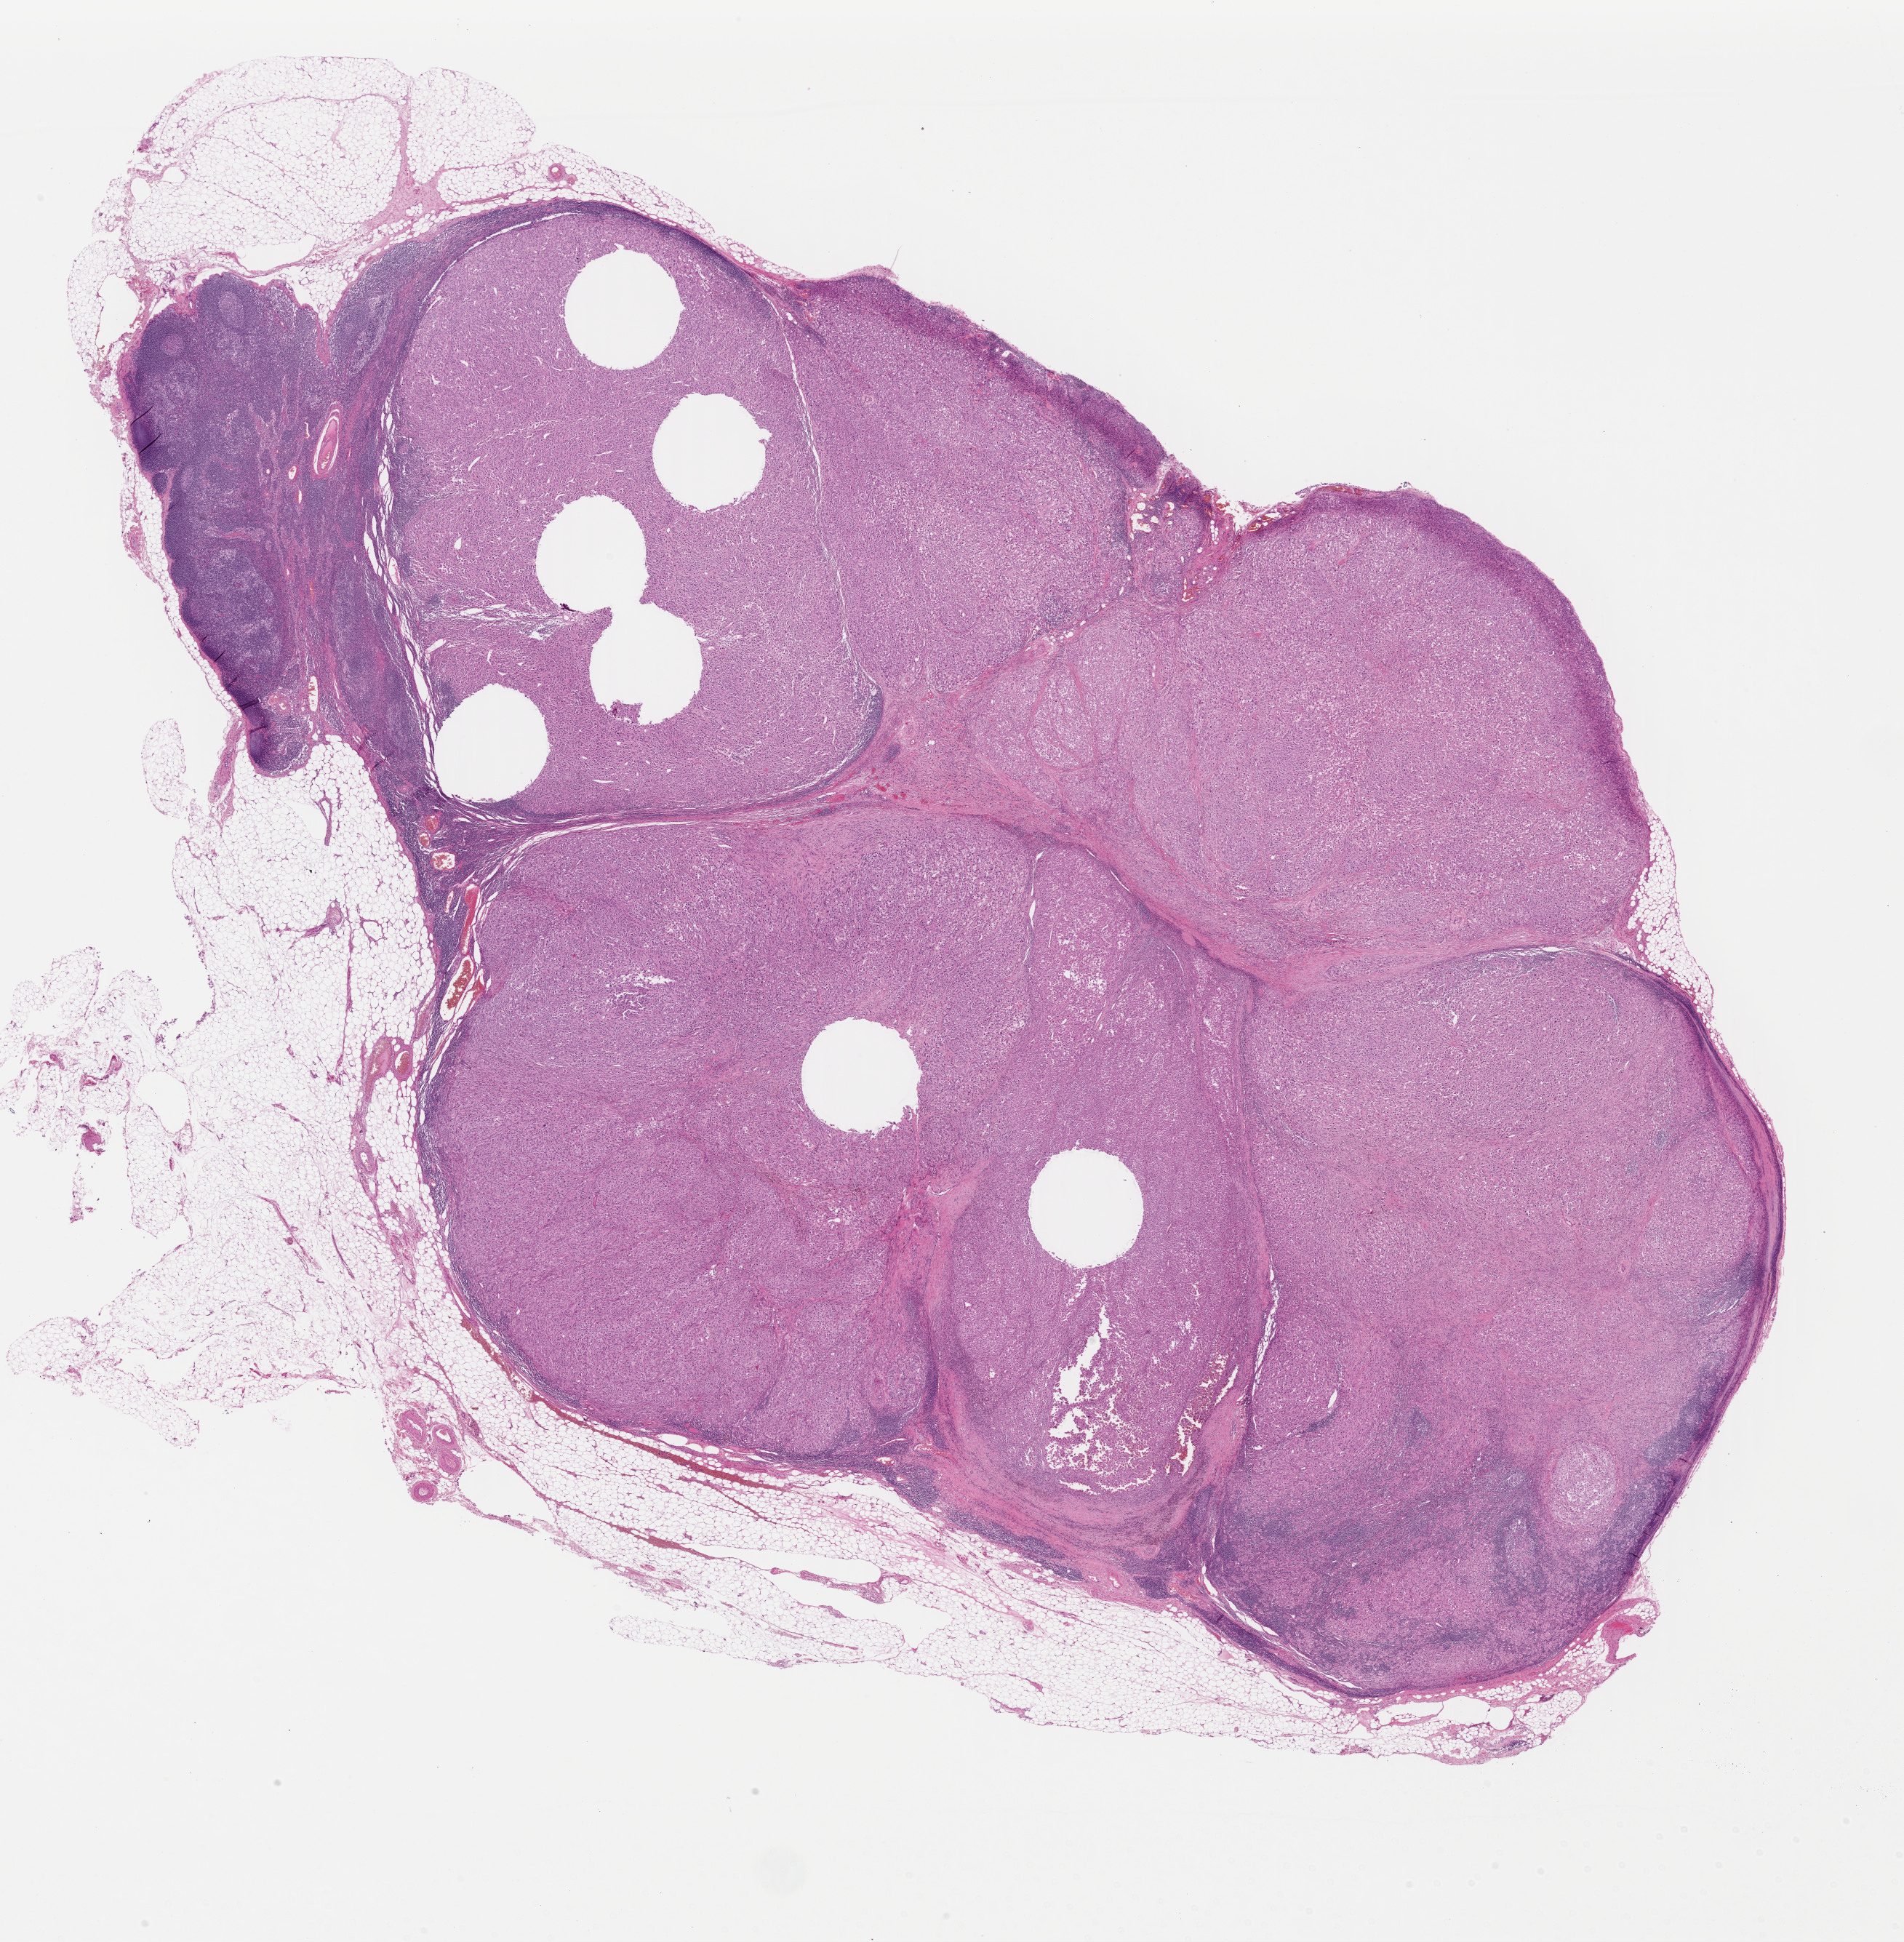
Whole-slide histology image, H&E, low-resolution overview of the scanned area, about 20.6 x 21.0 mm (from a 40x scan), FFPE section, skin, primary tumour sample. Patient: male, age at initial diagnosis 23 years.
Histologic diagnosis: Malignant melanoma, NOS.